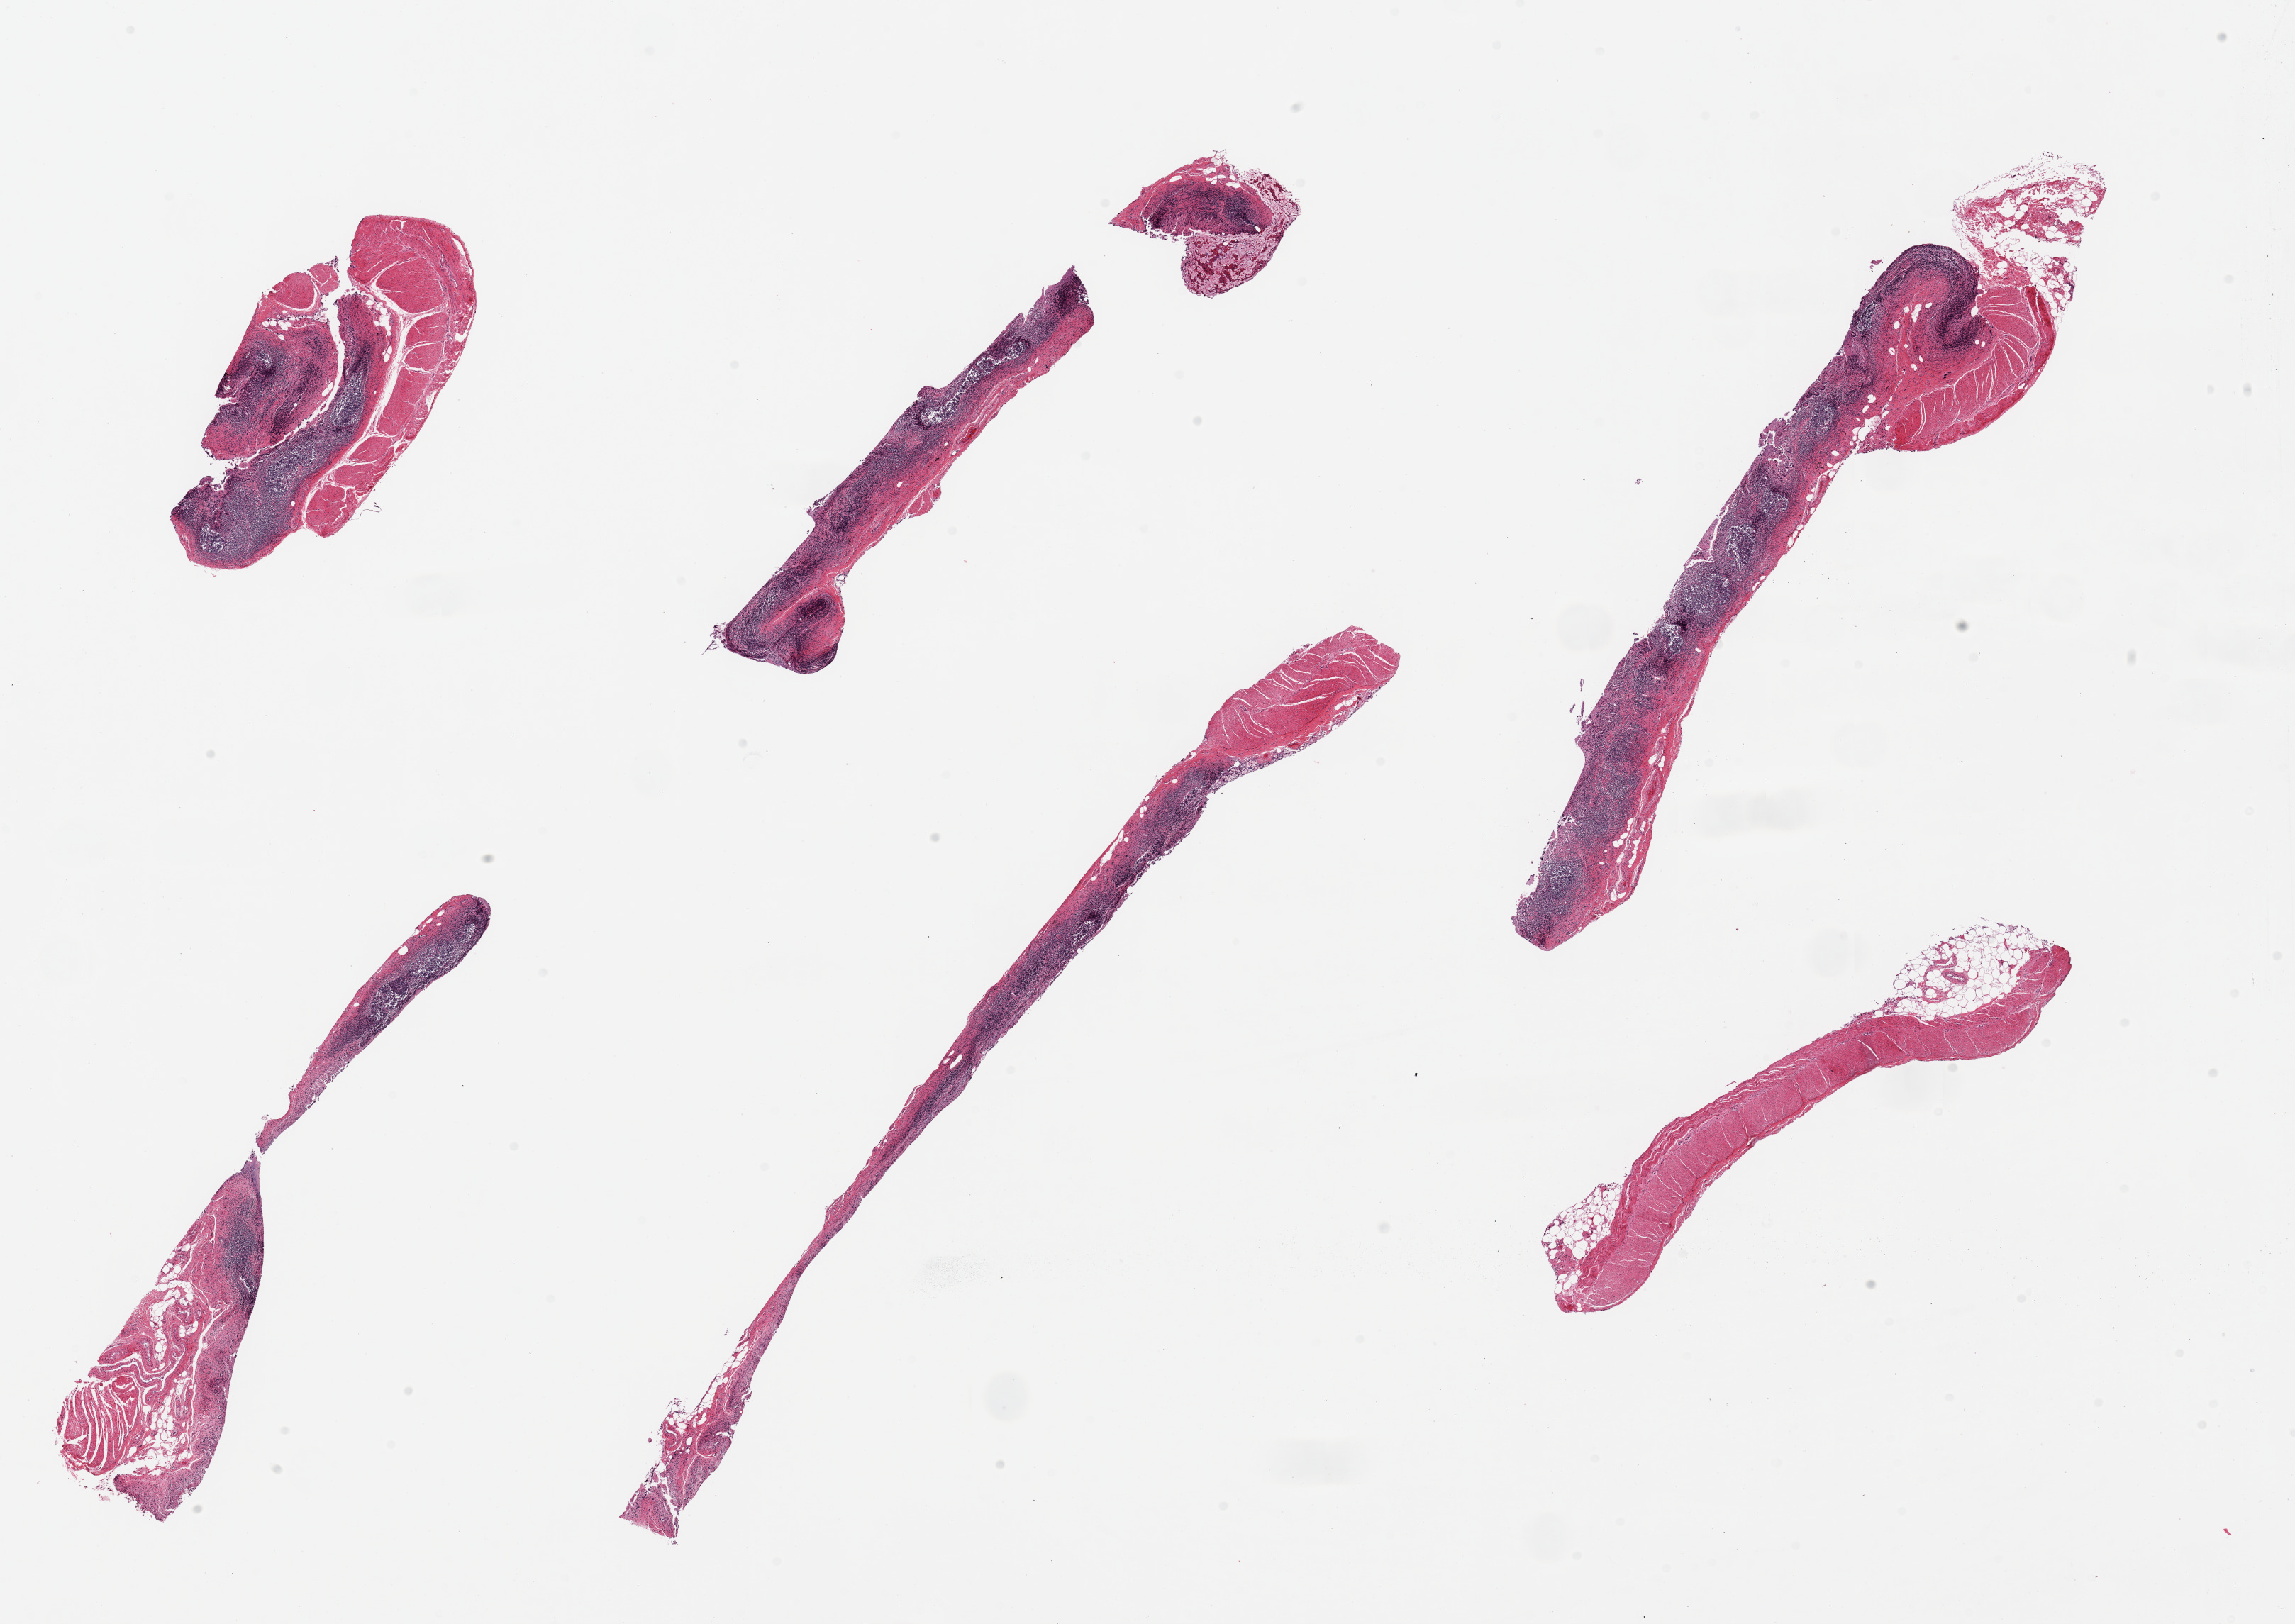
Digitized haematoxylin and eosin-stained section — low-resolution overview of the scanned area, about 25.6 x 18.1 mm (slide scanned at 20x), PAXgene-fixed paraffin-embedded (PFPE) section, section of ileum (target tissue), donor tissue sample. Donor: male.
Review note (as recorded): 6 pieces, glandular mucosa autolyzed but residual target lymphoid aggregates are ~40% of tissue.